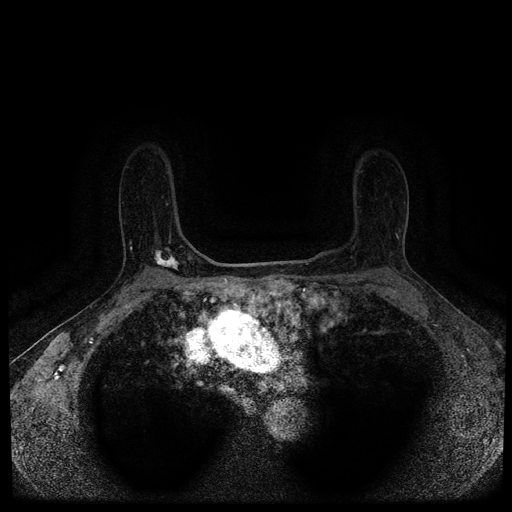
Breast MRI (dynamic contrast-enhanced, multi-phase), one axial slice; position 75 of 116 along the scan axis; dynamic contrast-enhanced series, time point 2 of 5 at this slice position (early post-contrast); 1.5 T; TE 2.7 ms, TR 5.4 ms; 512 × 512 image matrix, field of view 330 × 330 mm. Female patient, age 63 years.
Annotated regions visible in this slice (semi-automatically segmented with operator editing):
- breast lesion (labelled 'tumour' in the annotation; benign lesions carry a separate 'benign' label): bounding box (x1, y1, x2, y2) in pixels: (152, 250, 181, 272)